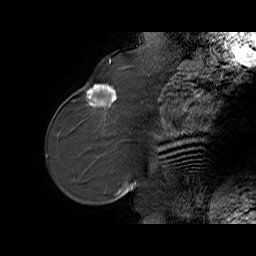
Breast MRI (dynamic contrast-enhanced), one sagittal slice. Dynamic contrast-enhanced series, time point 2 of 6 at this slice position (early post-contrast). 1.5 T. TE 5.7 ms, TR 32.9 ms. 4 mm slice thickness. 256 × 256 image matrix. Female patient. Case-level facts recorded for this patient, not image findings: setting: breast cancer imaged before/during neoadjuvant chemotherapy; receptor status: HER2-positive.
Annotated regions visible in this slice (semi-automatic segmentation, software-assisted and operator-edited):
- analysis volume of interest (the breast-tissue region the enhancement analysis was run in; not a lesion): bounding box <76,77,125,128> (left, top, right, bottom; pixels)
- tumour enhancement mask (voxels above the 100 % enhancement threshold inside the analysis volume of interest): <86,84,117,107>